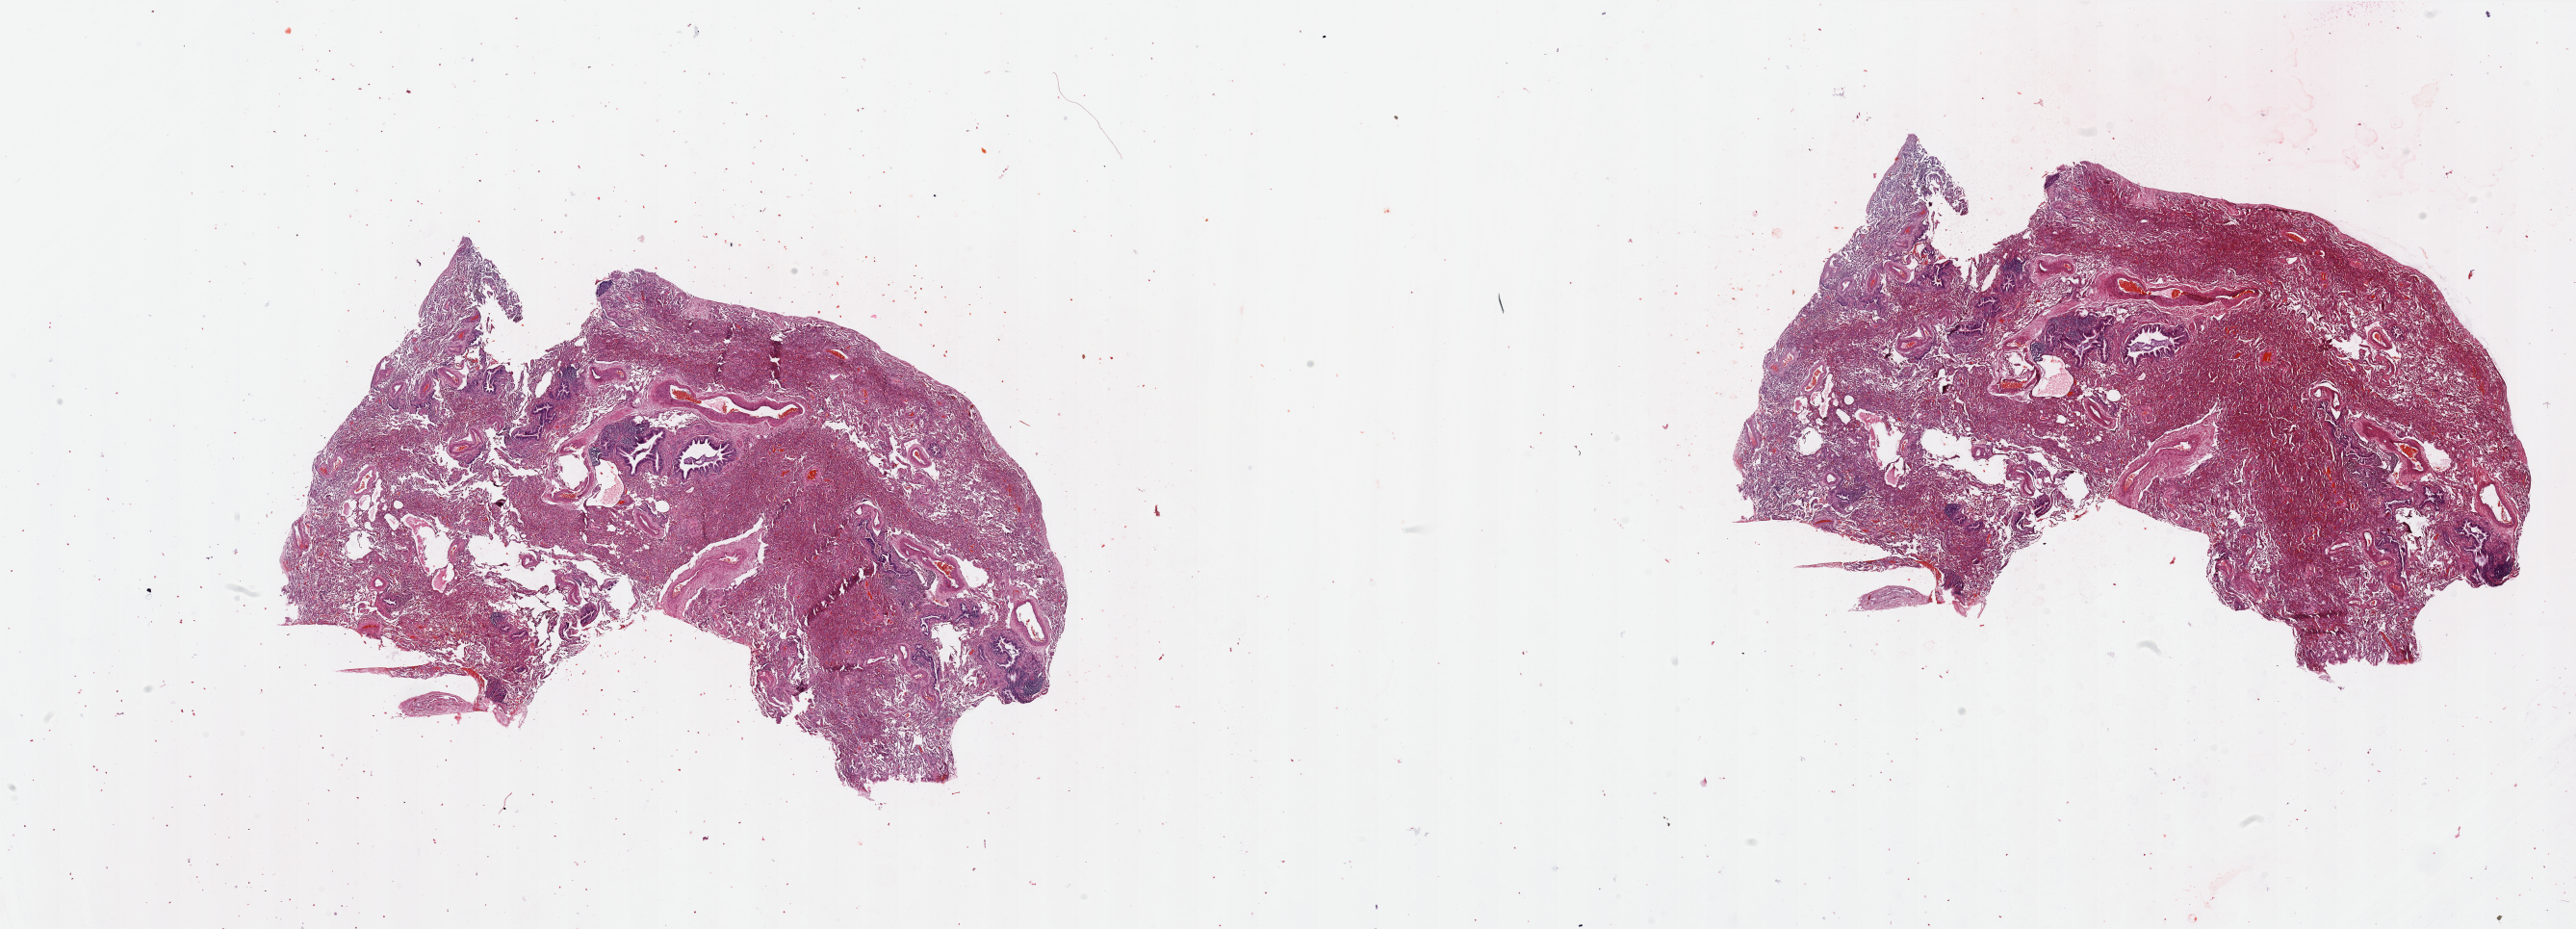
Digitized Hematoxylin and eosin (H&E) stained tissue section (whole slide), whole scanned area (about 42.3 x 15.3 mm, acquisition: 20x scan) shown as a low-resolution overview. Normal (non-tumour) tissue sample, sampled site: lung. Female, 64 y/o.
- this section: normal (non-tumour) tissue from the same patient
- patient diagnosis: Squamous cell carcinoma, NOS